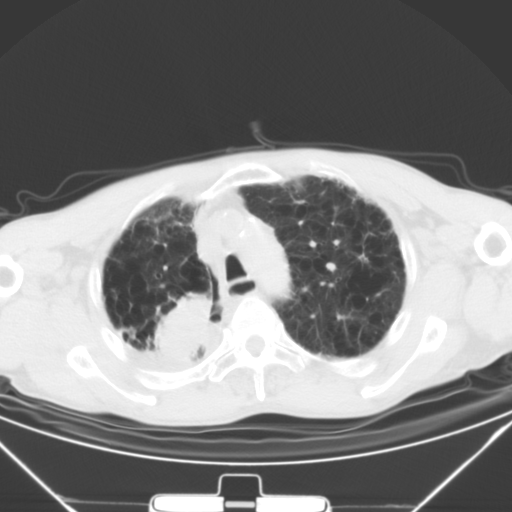
Chest CT, one axial slice. Slice 38 of 50 in the series (ordered by position). 120 kVp. Lung window (W 1500 / L -600 HU). 5 mm slice thickness. 512 × 512 image matrix. Male patient, age 65 years. From the clinical record (not read from this slice): clinical TNM (as recorded): T3 N1 M1a.
Structures marked on this image (rectangle marked by the reading radiologist):
- lung tumour (recorded histology: squamous cell carcinoma): bounding box [x1, y1, x2, y2] px = [148, 294, 219, 354]